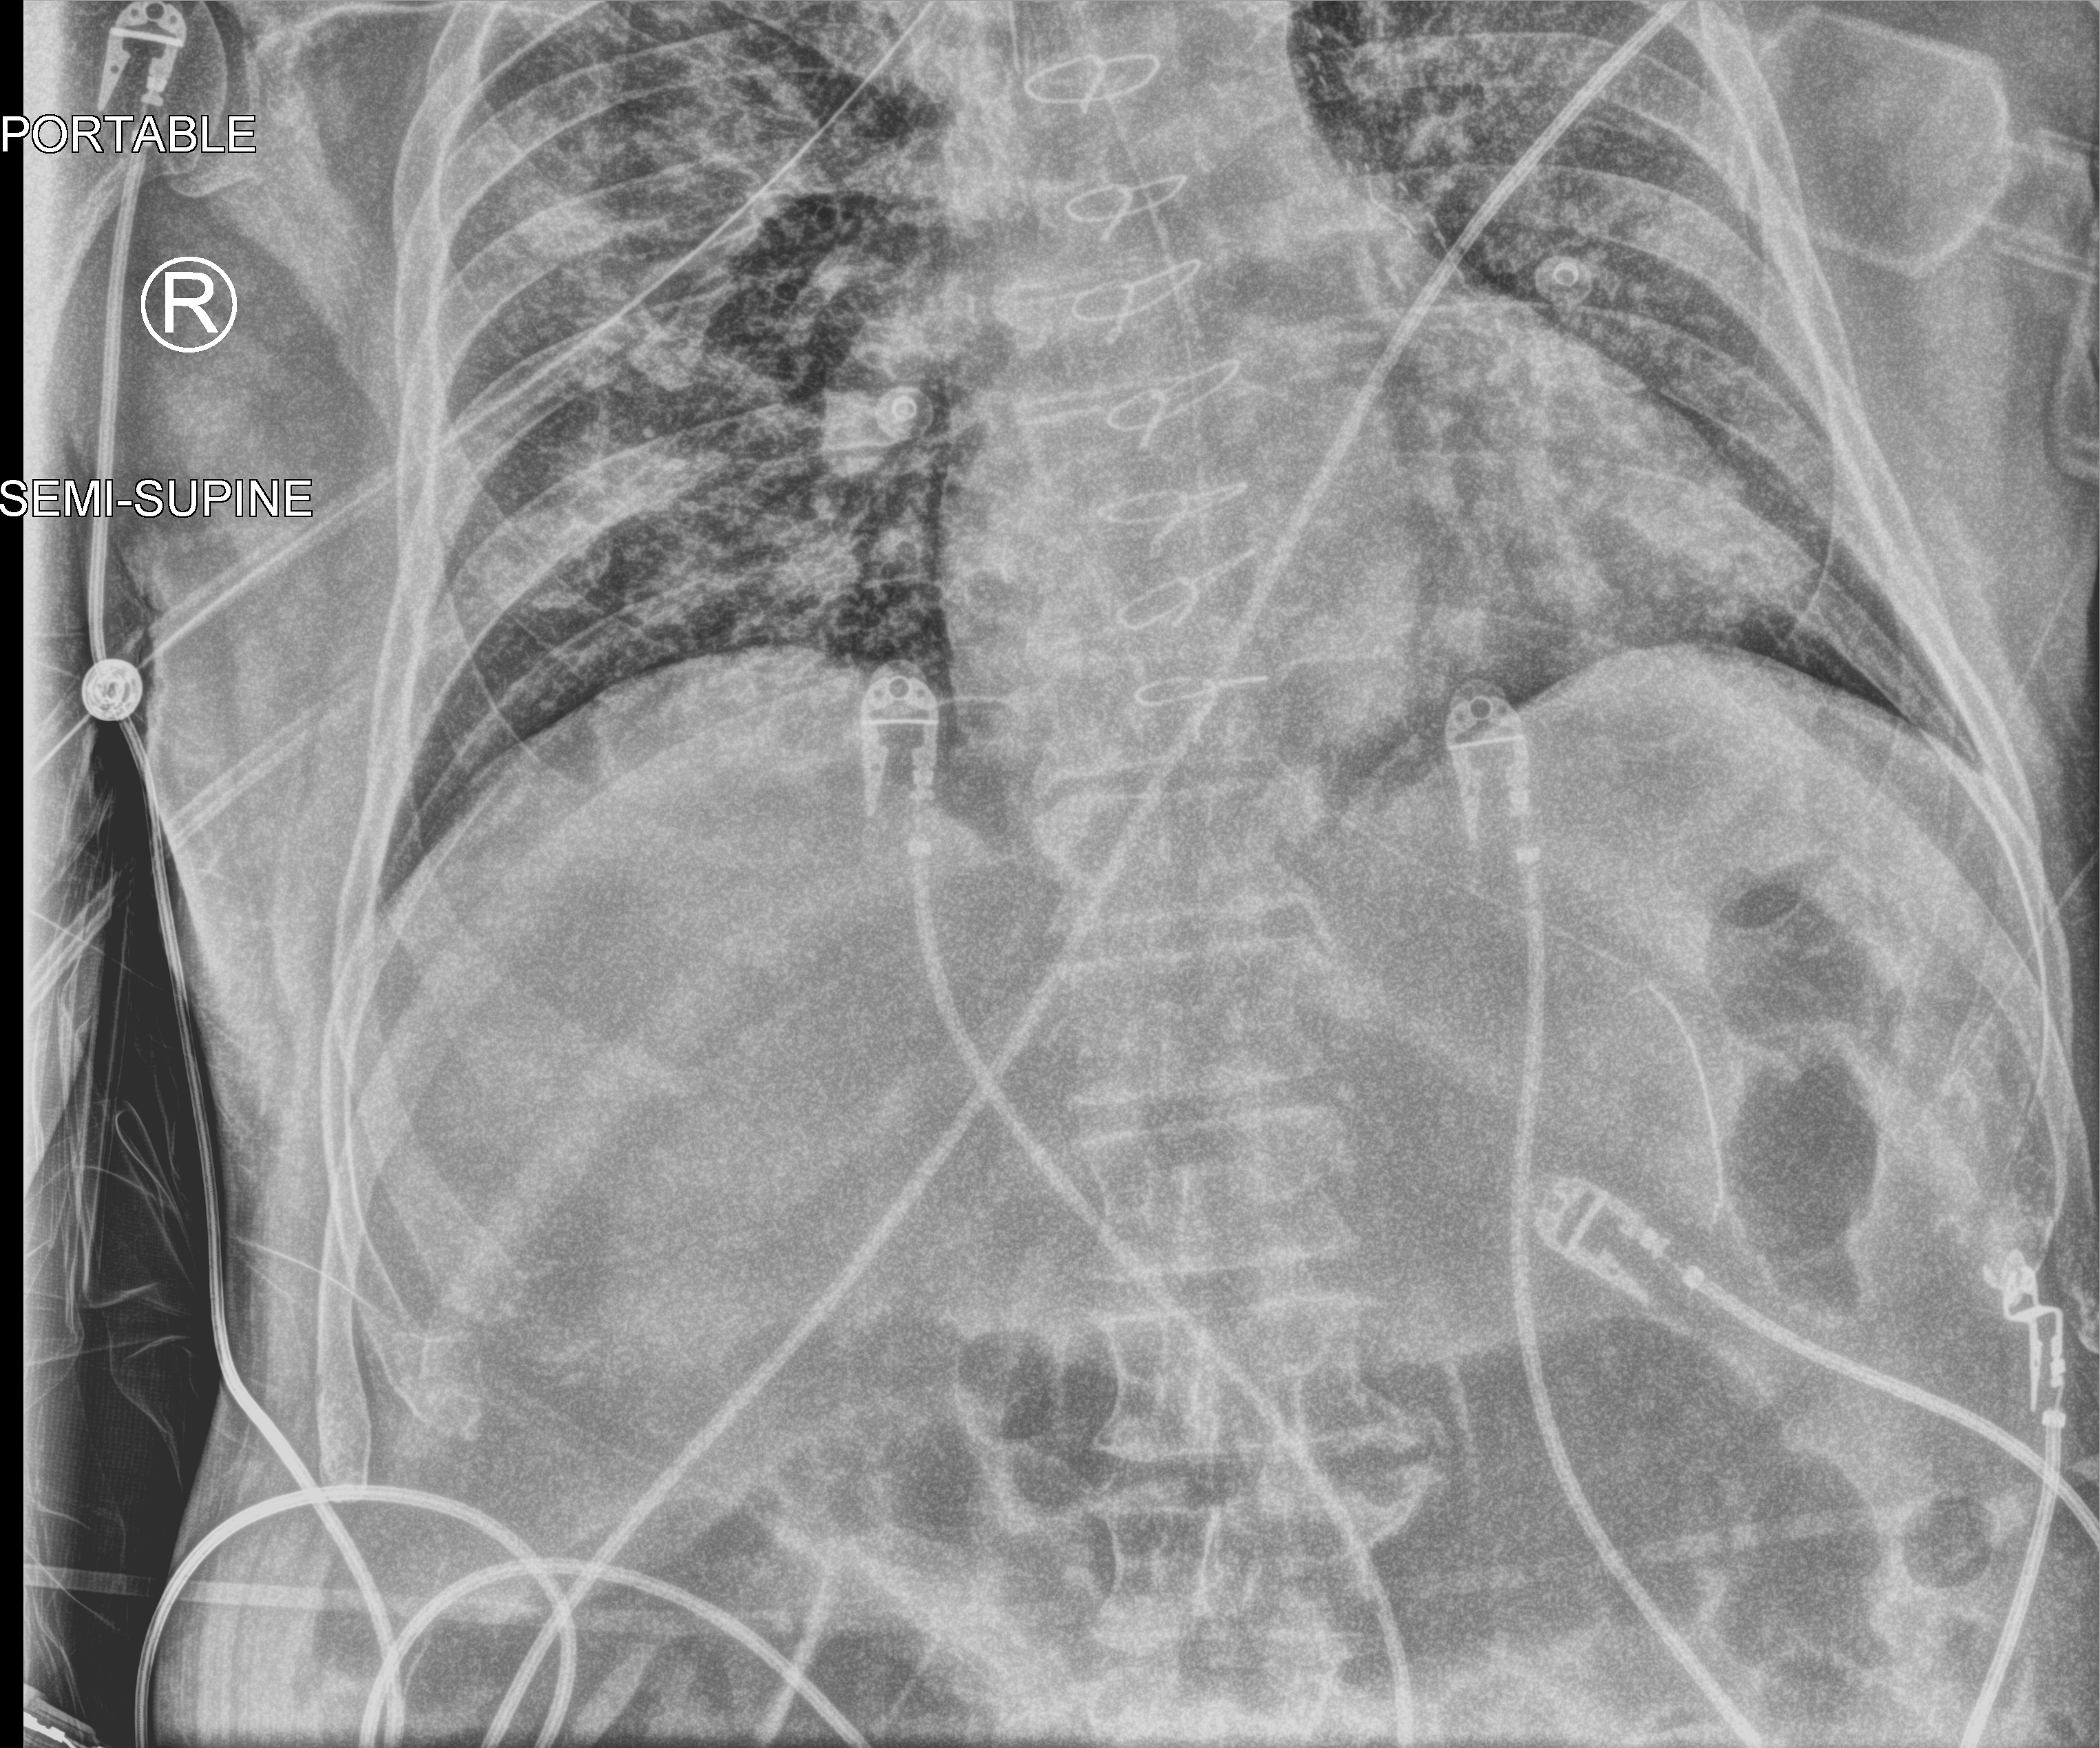
Portable chest radiograph, anteroposterior (AP) projection. Patient hospitalised with COVID-19; male, aged 60–74 years.
Admission-level facts for this patient (not findings on this image; timing relative to this image not recorded): length of hospital stay: 22 days; mechanically ventilated during this hospital stay: yes; admitted to intensive care during this hospital stay: yes.